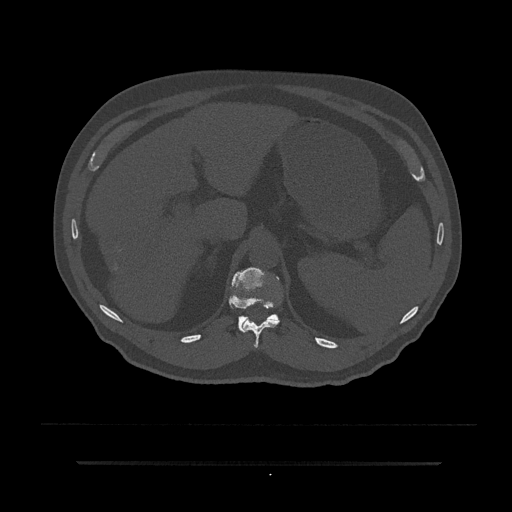
CT including the spine, one axial slice. Slice 241 of 797 in the series (ordered by position). Bone window (W 1800 / L 400 HU). 512 × 512 image matrix, field of view 464 × 464 mm. Male patient, age 59 years. Case-level facts recorded for this patient, not image findings: primary cancer: bile ducts; vertebrae with lytic lesions (as recorded): T10.
Structures marked on this image (semi-automatically segmented with operator editing):
- T11 vertebra: bounding box (x1, y1, x2, y2) in pixels: (242, 319, 280, 349)
- T12 vertebra: (229, 267, 280, 333)